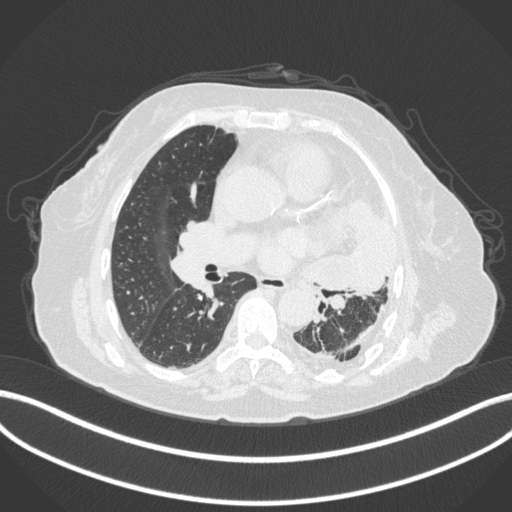
Chest CT, one axial slice; slice 192 of 399 in the series (ordered by position); reconstruction kernel B31f; lung window (W 1500 / L -600 HU); 1 mm slice thickness; 512 × 512 image matrix. Patient: female, 75 years. From the clinical record (not read from this slice): clinical TNM (as recorded): T3 N3 M1.
Annotated regions visible in this slice (rectangle marked by the reading radiologist):
- lung tumour (recorded histology: adenocarcinoma): bounding box <307,197,399,303> (left, top, right, bottom; pixels)